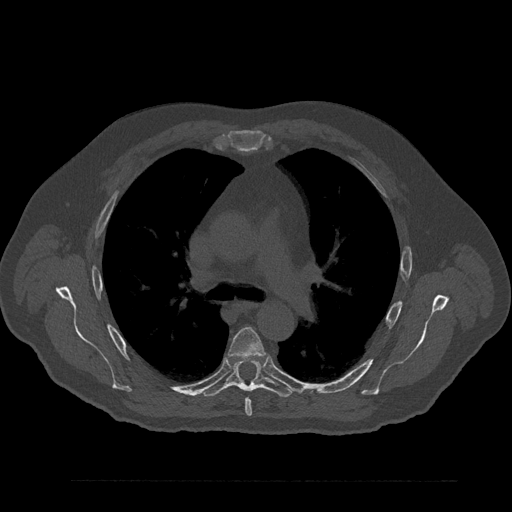
CT including the spine, one axial slice. Slice 577 of 797 in the series (ordered by position). Reconstruction kernel Br40s/3. 120 kVp. Bone window (W 1800 / L 400 HU). 512 × 512 image matrix, field of view 430 × 430 mm. Patient: male, 61 years. Case-level facts recorded for this patient, not image findings: primary cancer: prostate.
Outlined on this slice (semi-automatic segmentation, software-assisted and operator-edited):
- T5 vertebra: bounding box [x1, y1, x2, y2] px = [228, 328, 265, 416]
- T6 vertebra: [202, 357, 293, 397]